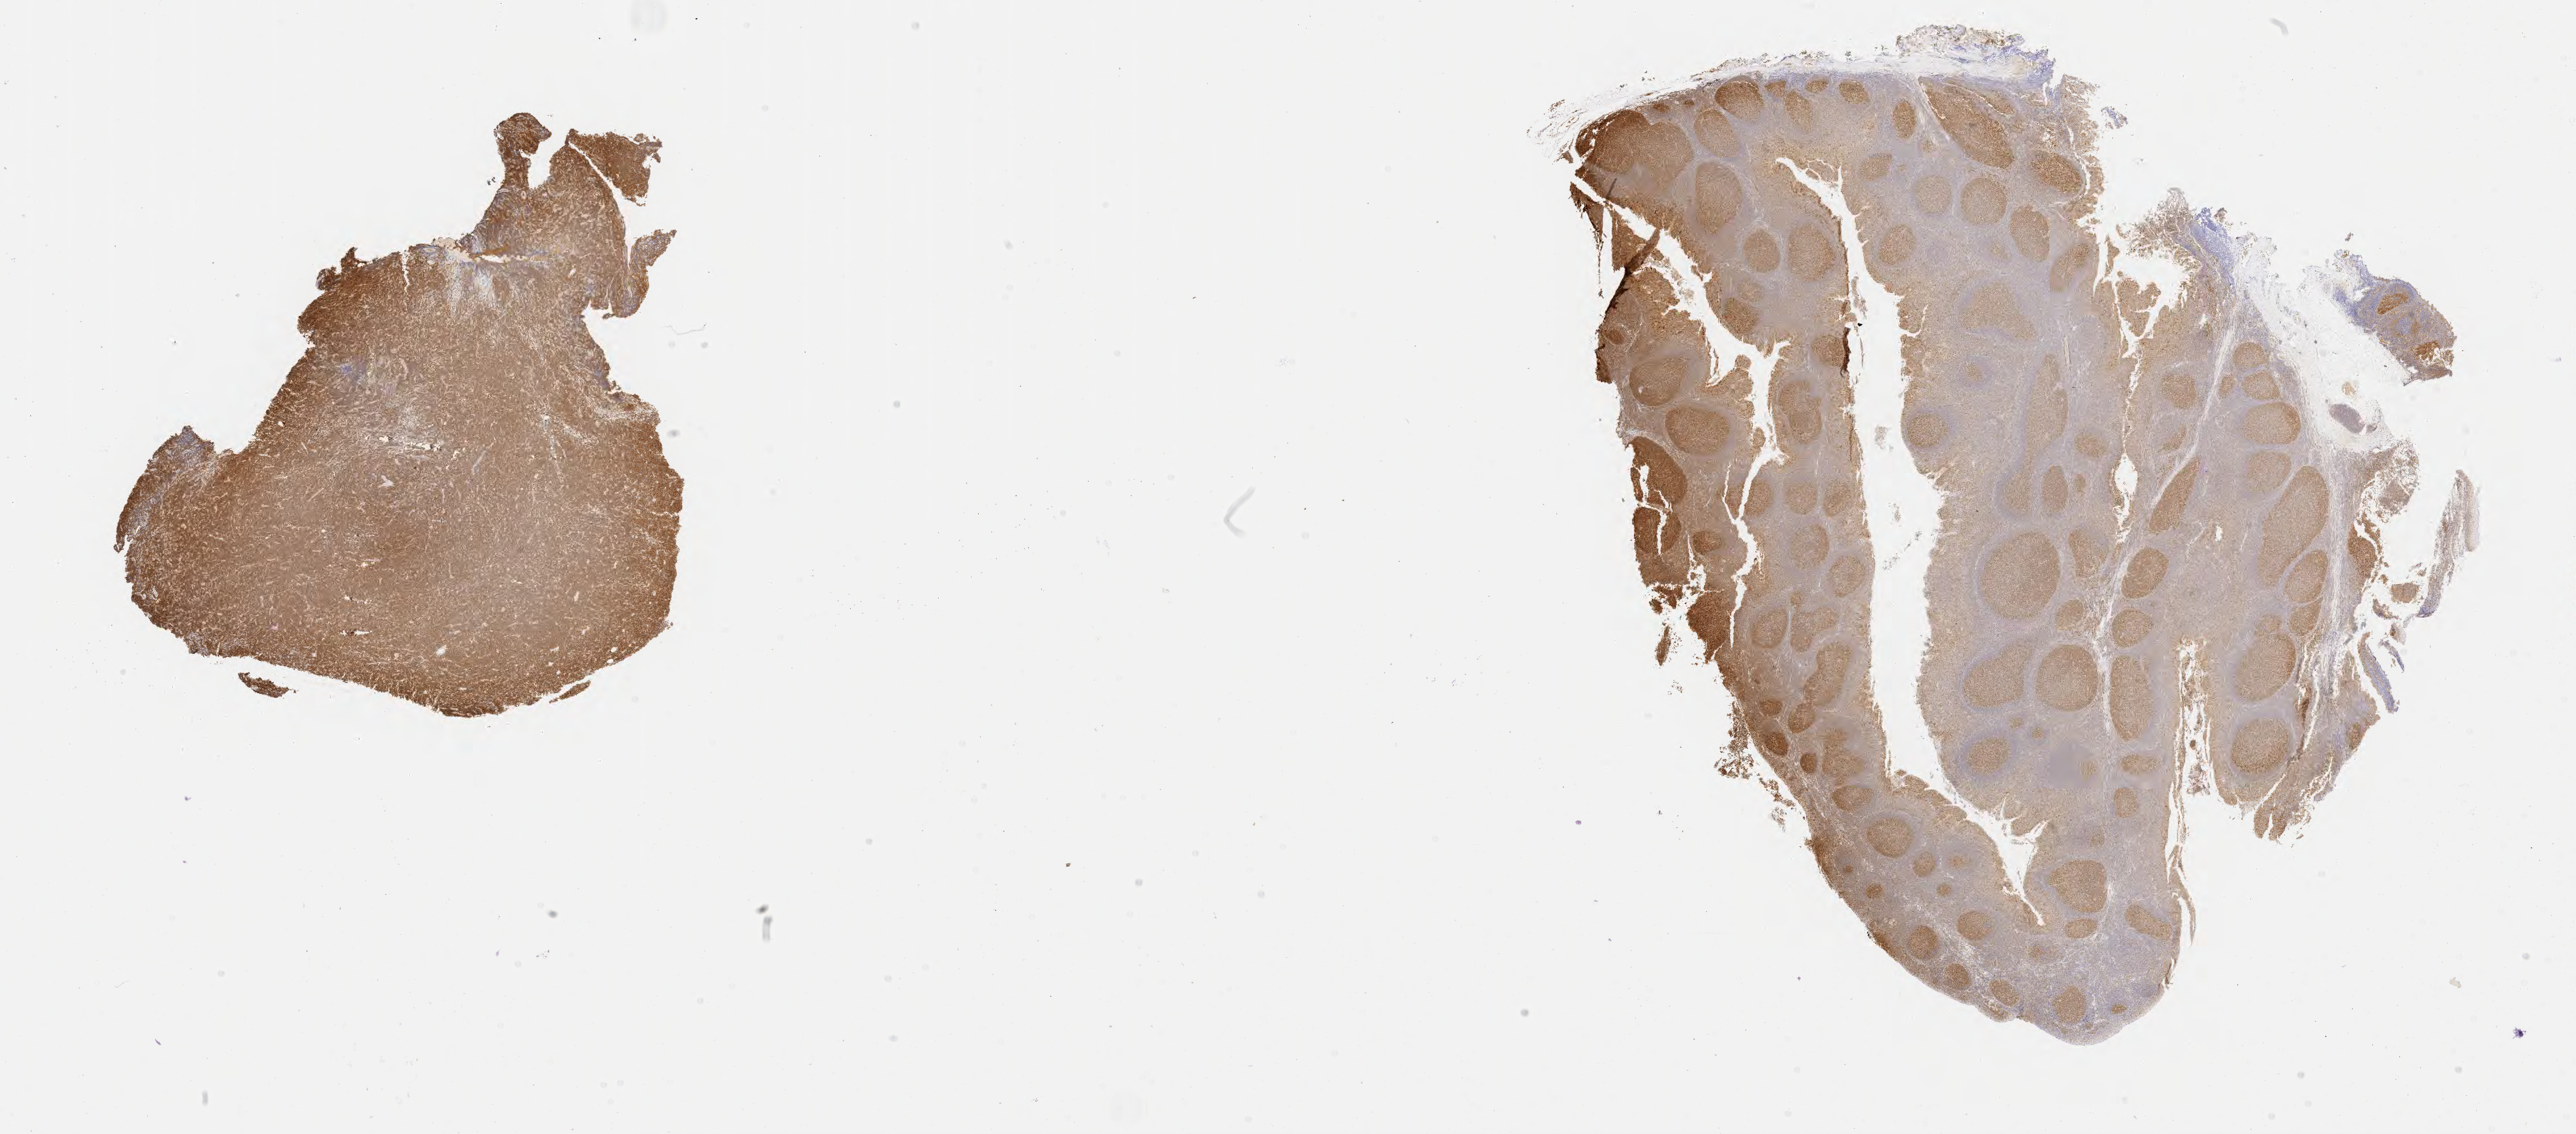
Whole-slide image, immunohistochemical stain for BCL6, shown as a low-resolution overview of the whole scanned area (about 31.7 x 14.0 mm), tumor tissue, anatomic site: mandible. Female patient; age at initial diagnosis 5 years.
Diagnosis: Burkitt lymphoma, NOS.